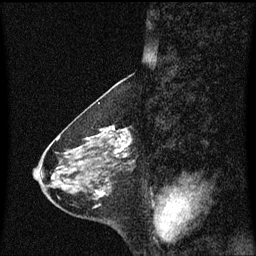
Breast MRI (dynamic contrast-enhanced), one sagittal slice. Position 26 of 60 along the scan axis. Dynamic contrast-enhanced series, image 2 of 3 at this slice position (ordered by acquisition). 1.5 T. TE 4.2 ms, TR 8.4 ms. 256 × 256 image matrix. Patient: female, 58 years.
Annotated regions visible in this slice (semi-automatic segmentation, software-assisted and operator-edited):
- analysis volume of interest (the breast-tissue region the enhancement analysis was run in; not a lesion): bounding box [x1, y1, x2, y2] px = [100, 126, 133, 160]
- tumour enhancement mask (voxels above the 70 % enhancement threshold inside the analysis volume of interest): [102, 126, 133, 157]